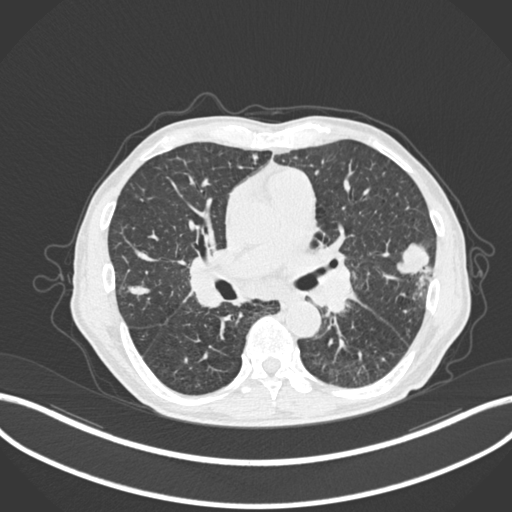
Chest CT, one axial slice. Position 126 of 287 along the scan axis. Reconstruction kernel B30f. 120 kVp. Lung window (W 1500 / L -600 HU). 512 × 512 image matrix. Patient: male, 74 years. Case-level facts recorded for this patient, not image findings: clinical TNM (as recorded): T2a N1 M0.
Structures marked on this image (bounding box drawn by a radiologist):
- lung tumour (recorded histology: adenocarcinoma): box from (x=393, y=238) to (x=433, y=289) px